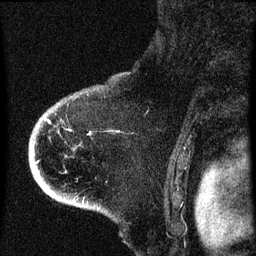
Breast MRI (dynamic contrast-enhanced), one sagittal slice. Slice 52 of 60 in the series (ordered by position). Dynamic contrast-enhanced series, image 2 of 4 at this slice position (ordered by acquisition). 1.5 T. TE 4.2 ms, TR 8 ms. 256 × 256 image matrix, field of view 180 × 180 mm. Patient: female, 71 years.
Structures marked on this image (semi-automatic segmentation, software-assisted and operator-edited):
- analysis volume of interest (the breast-tissue region the enhancement analysis was run in; not a lesion): box from (x=32, y=86) to (x=108, y=205) px
- tumour enhancement mask (voxels above the 70 % enhancement threshold inside the analysis volume of interest): (x=37, y=120)–(x=71, y=163)